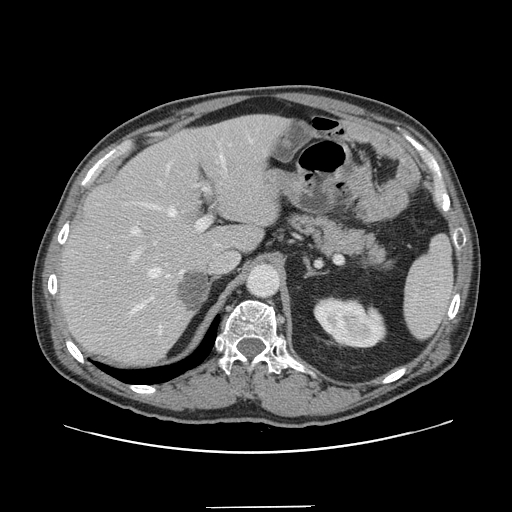
Contrast-enhanced abdominal CT, one axial slice; intravenous contrast given; soft-tissue window (W 400 / L 40 HU); 2.5 mm slice thickness; 512 × 512 image matrix, field of view 397 × 397 mm. Male patient, age 64 years. From the clinical record (not read from this slice): diagnosis: colorectal cancer liver metastases, imaged before liver resection; multiple liver metastases: yes; largest metastasis: 3.5 cm; disease in both lobes: yes.
Outlined on this slice (manually delineated by an expert):
- hepatic veins: bounding box <130,138,253,334> (left, top, right, bottom; pixels)
- liver: <61,116,284,364>
- planned liver remnant (the part of the liver to remain after resection): <61,116,274,364>
- portal vein (with intrahepatic branches): <131,144,231,274>
- liver metastasis: <179,272,208,313>